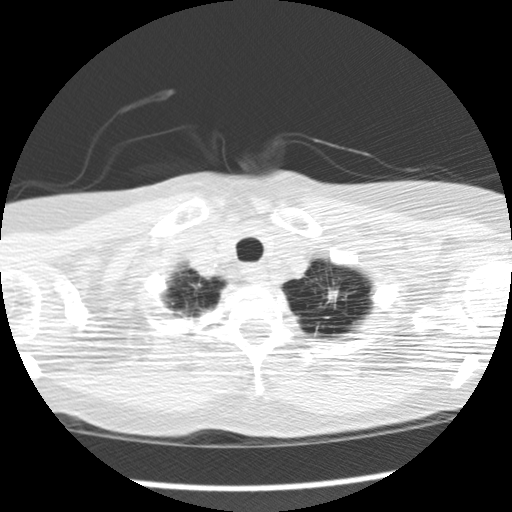
Low-dose screening chest CT, one axial slice; reconstruction kernel STANDARD; lung window (W 1500 / L -600 HU); 2.5 mm slice thickness; 512 × 512 image matrix, field of view 308 × 308 mm.
Structures marked on this image (manually delineated by an expert):
- lesion 1 (tumor, upper lobe of left lung): bounding box [x1, y1, x2, y2] px = [327, 289, 339, 303]